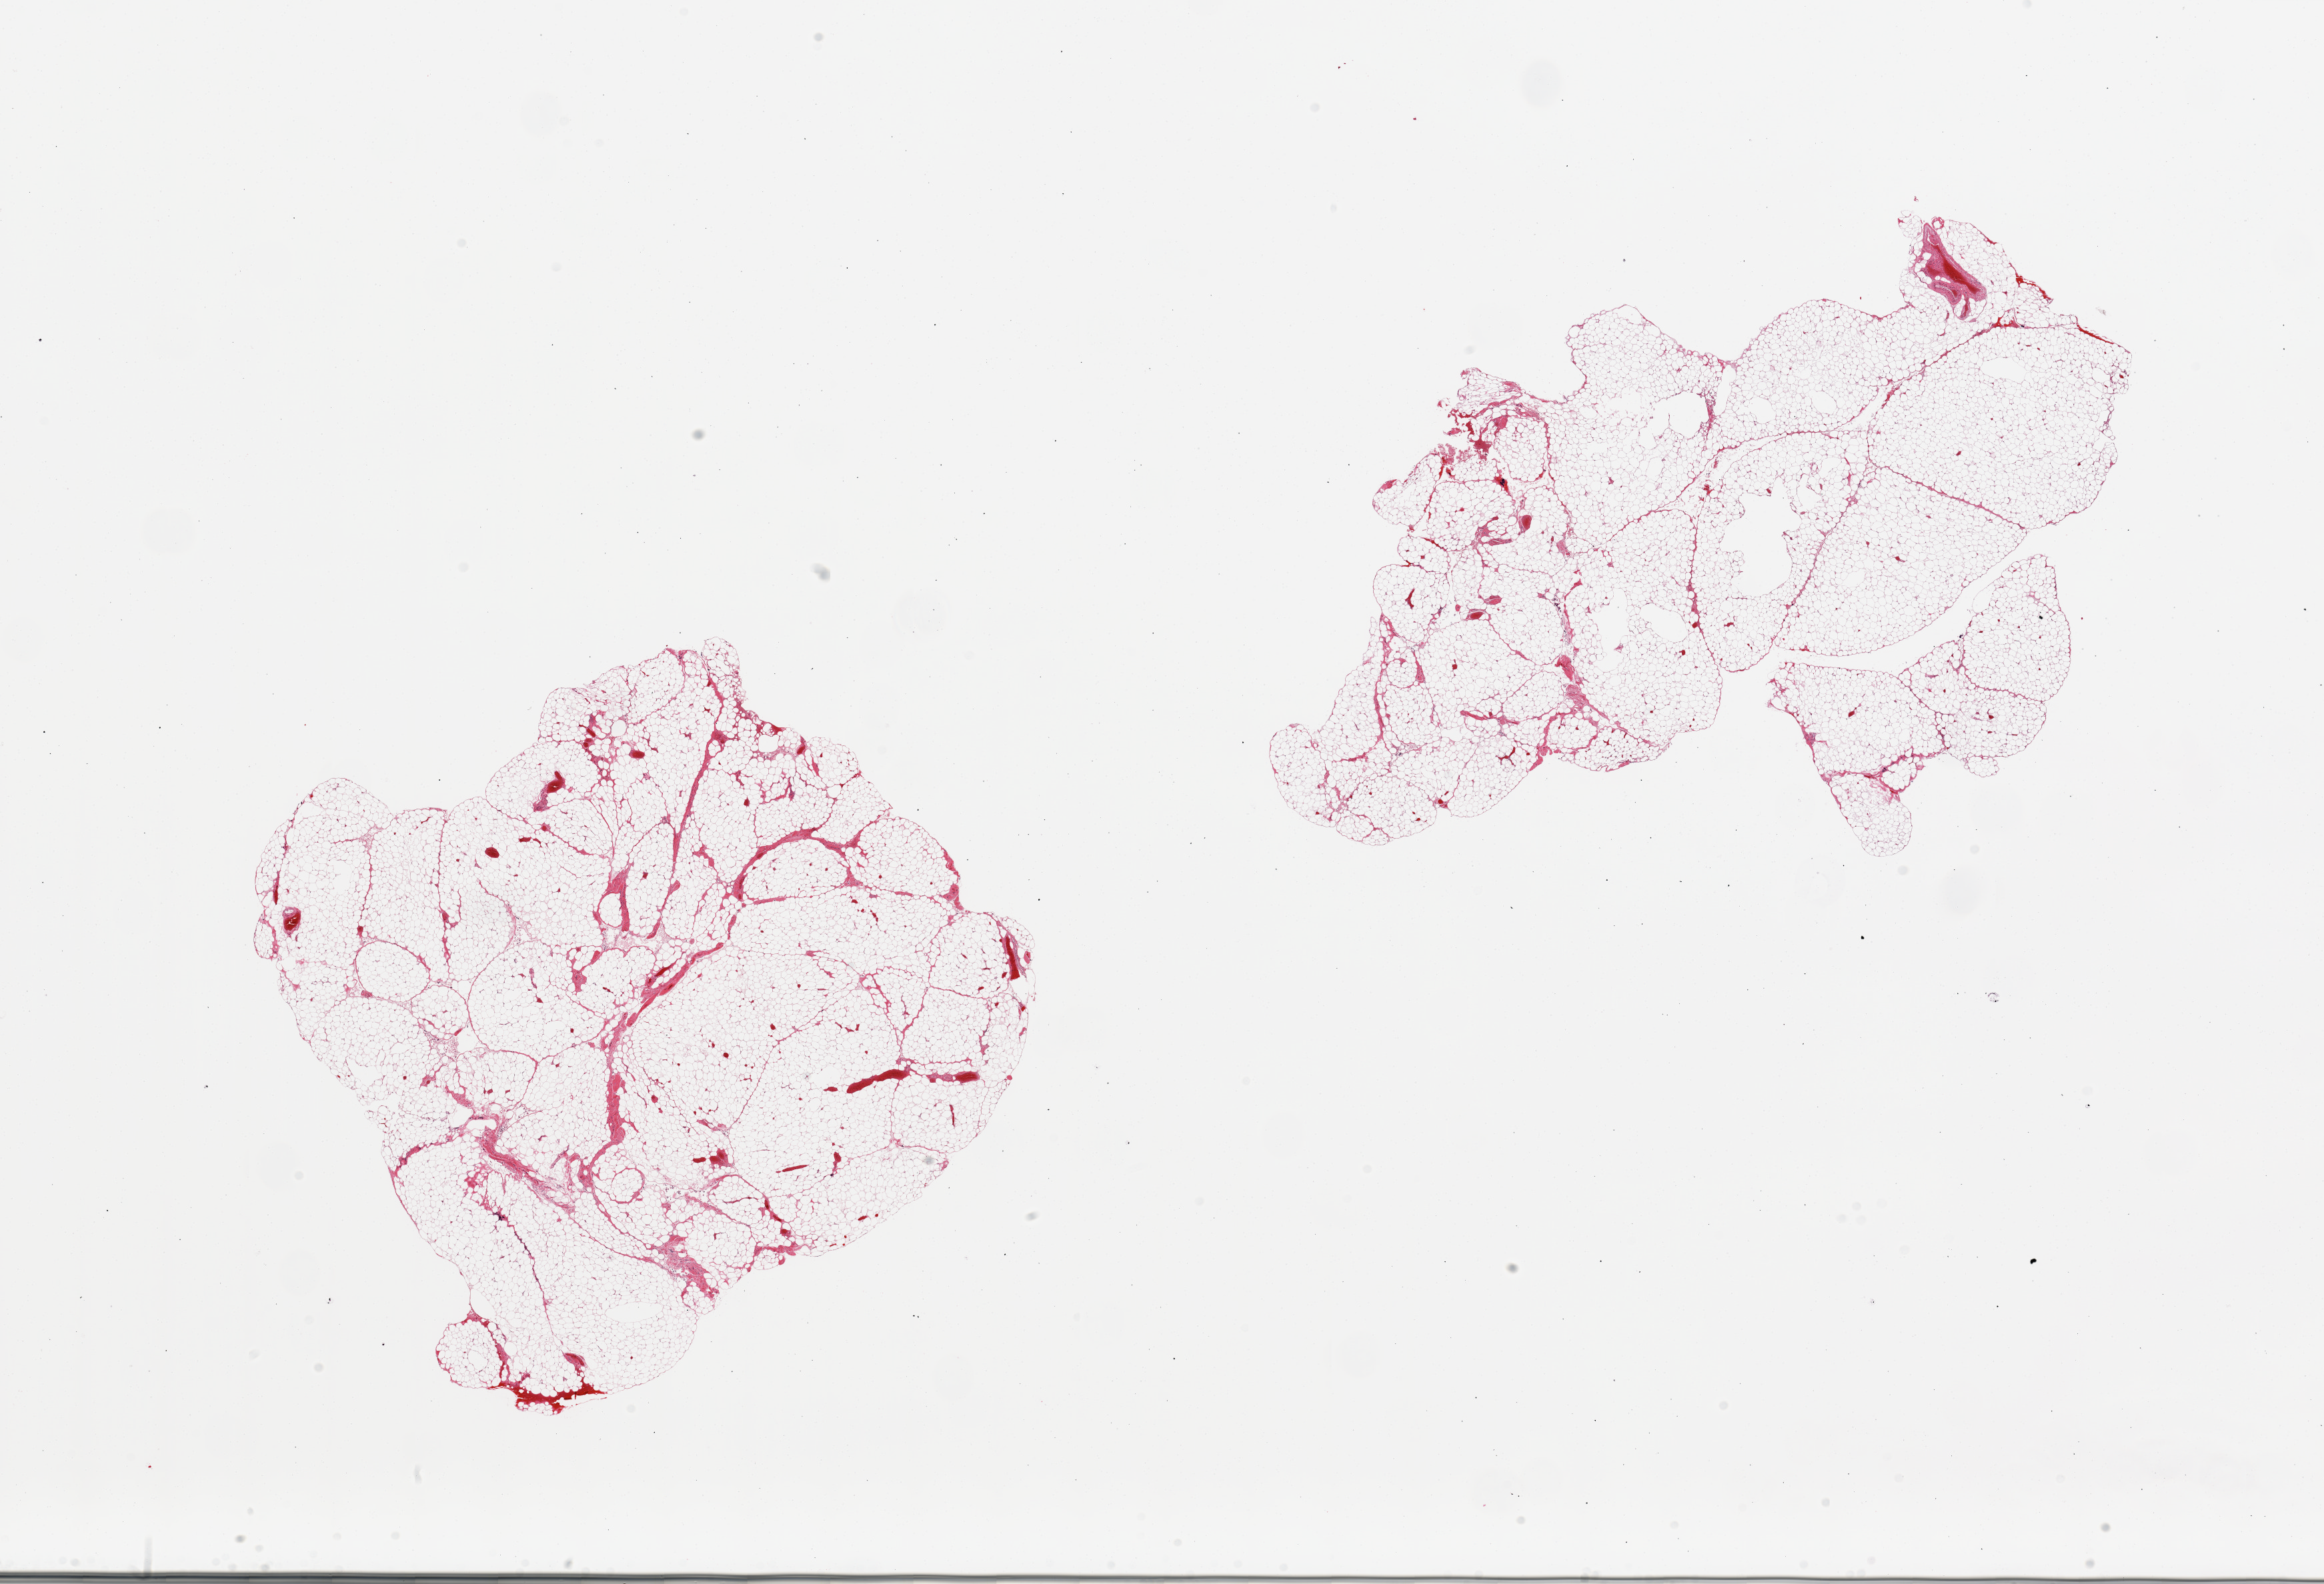
Haematoxylin and eosin whole-slide image, brightfield, whole scanned area (about 27.6 x 18.8 mm) shown as a low-resolution overview; PAXgene-fixed, paraffin-embedded tissue; target tissue: omentum; tissue donor sample. Female donor.
Review note (as recorded): 2 pieces; 1% fibrous content.